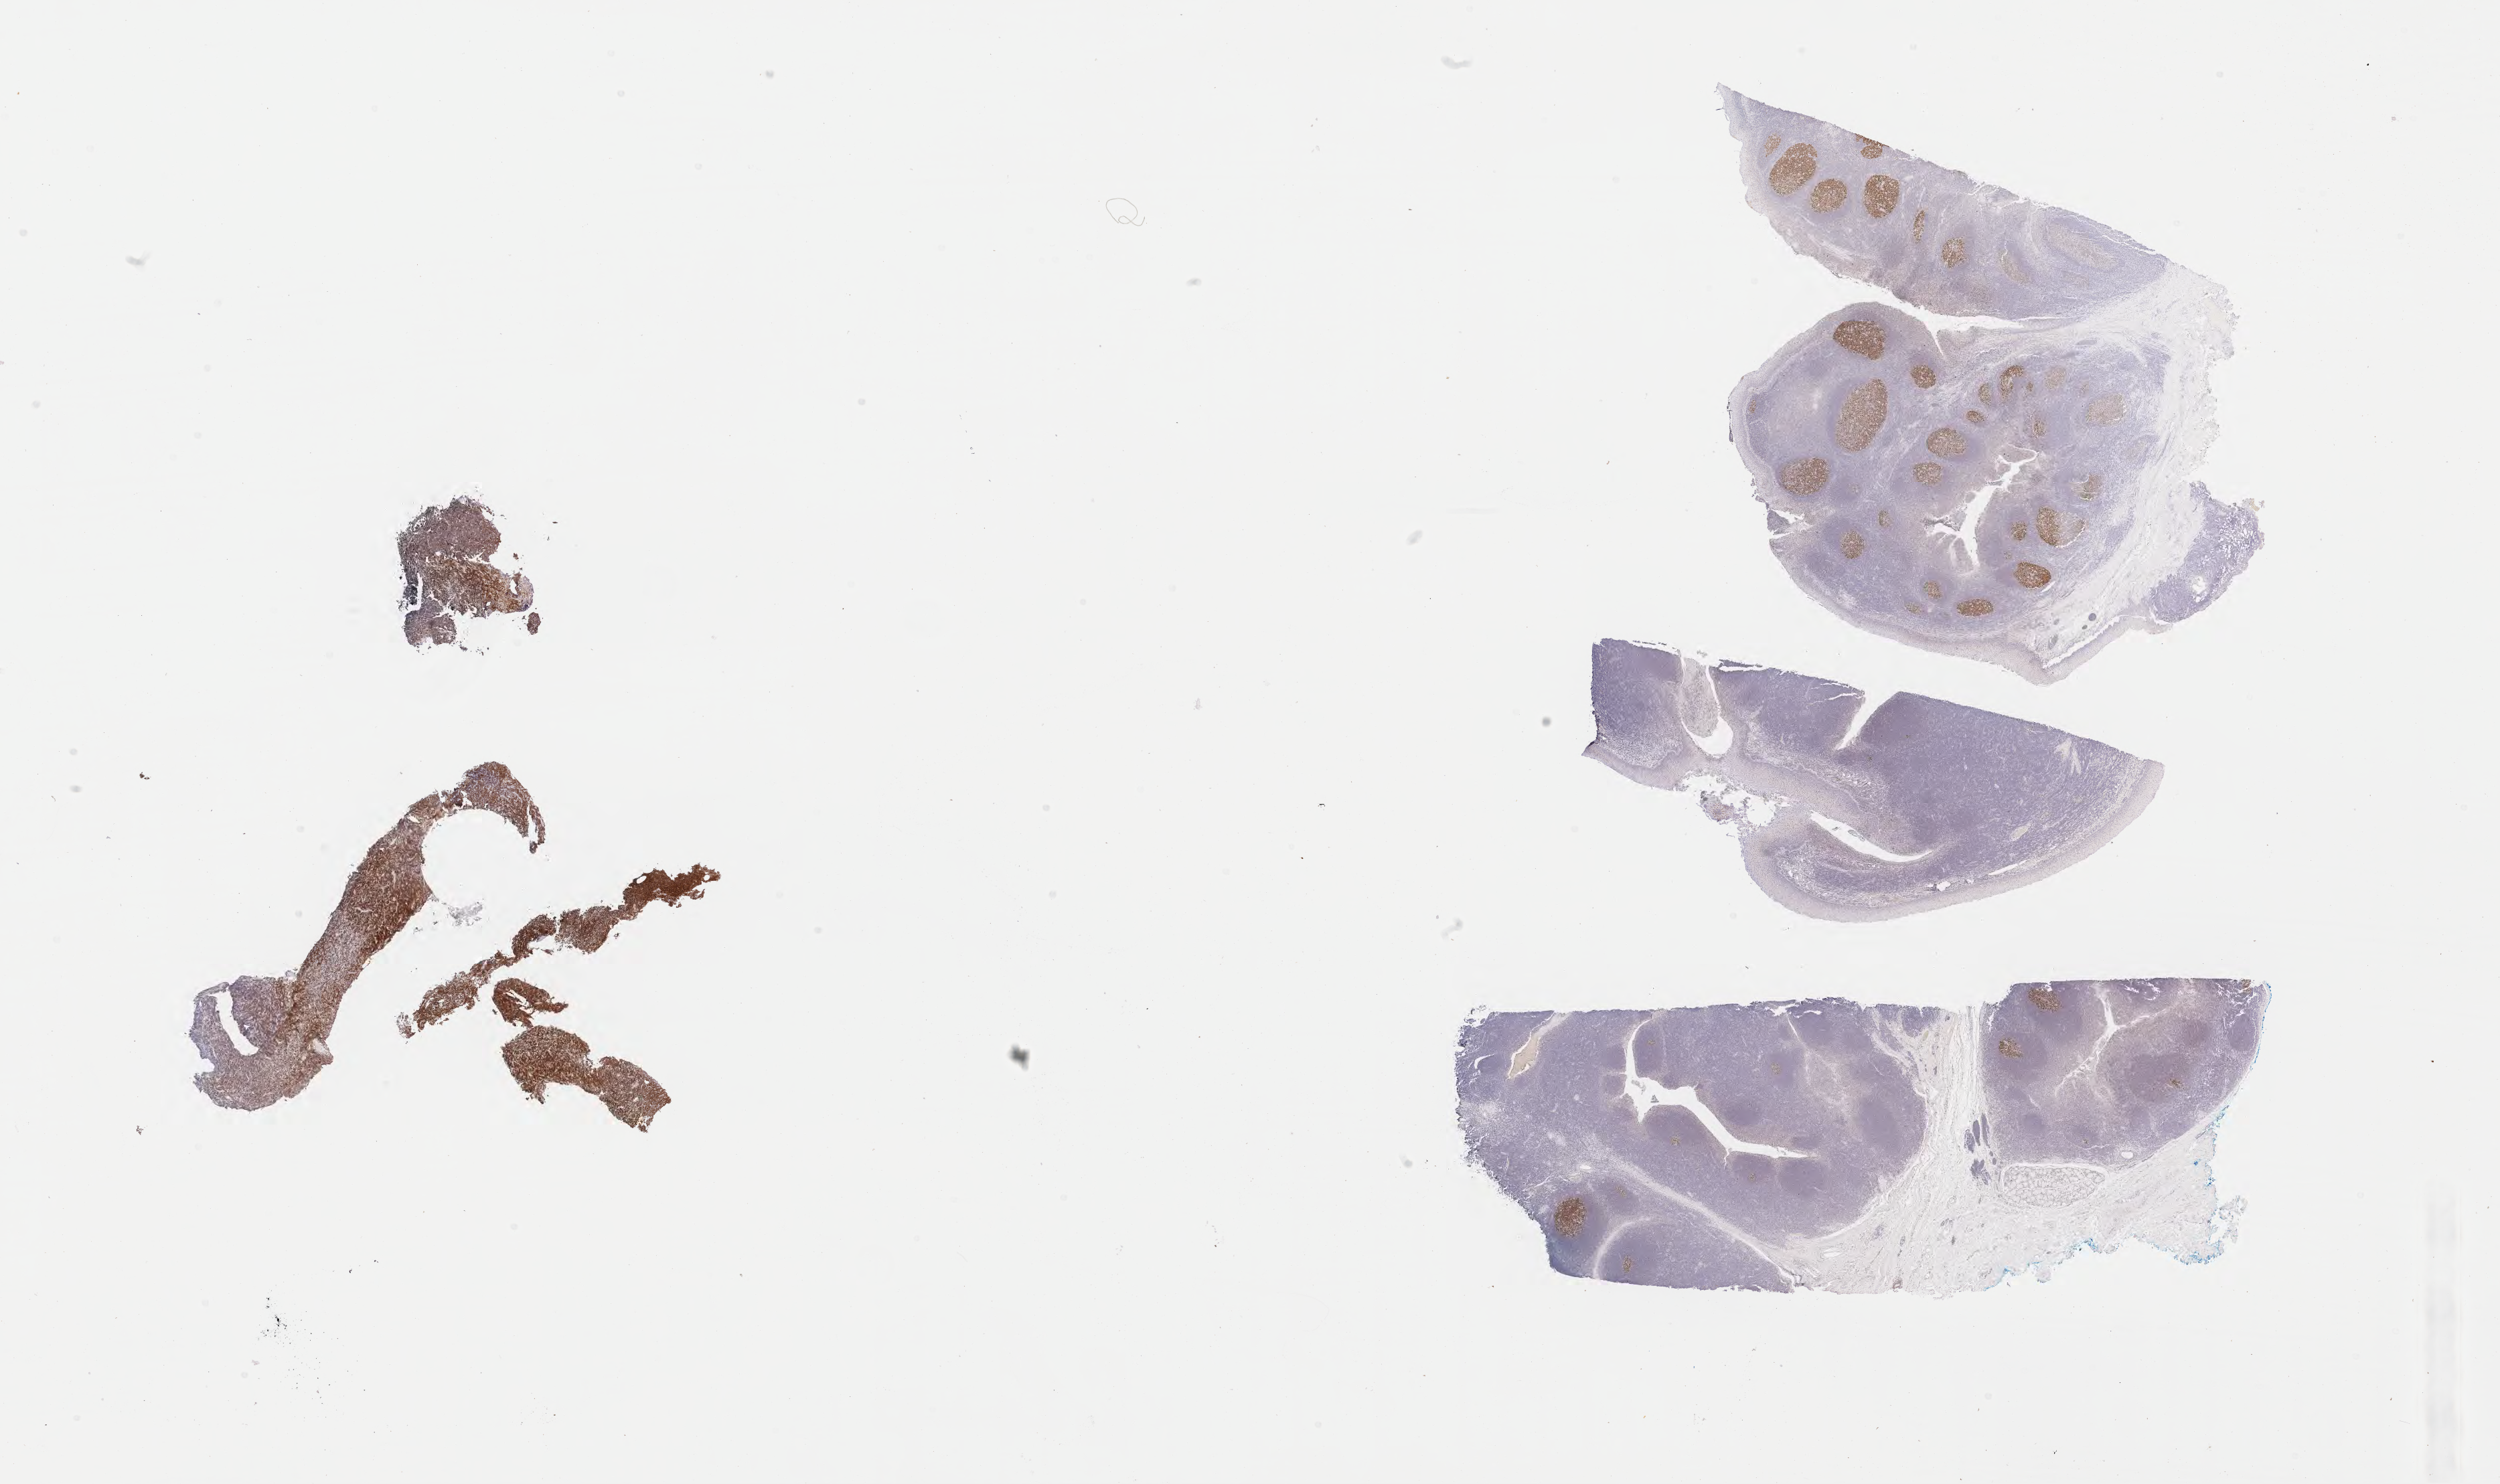
IHC for BCL6, whole-slide image — whole scanned area (about 30.2 x 17.9 mm) shown as a low-resolution overview, specimen: tumor tissue, anatomic site: cranium. Male patient; age at initial diagnosis 5 years.
- diagnosis: Burkitt lymphoma, NOS